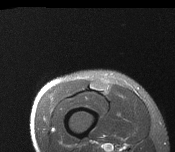
MRI of an extremity soft-tissue mass, one axial slice. Slice 28 of 116 in the series (ordered by position). T2-weighted fat-saturated. MR volume resampled by the dataset authors to the PET/CT grid (not the native acquisition matrix). 3.27 mm slice thickness. 175 × 152 image matrix, field of view 171 × 148 mm. Male patient. Case-level facts recorded for this patient, not image findings: histological type: pleiomorphic leiomyosarcoma; grade: intermediate; site of the primary tumour: right thigh.
Annotated regions visible in this slice (expert contour drawn on MRI and transferred to this co-registered scan by the dataset authors):
- gross tumour volume including surrounding oedema: box from (x=93, y=84) to (x=103, y=89) px